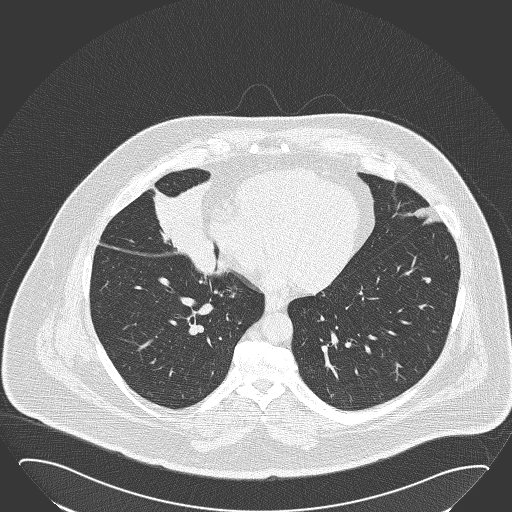
Low-dose screening chest CT, one axial slice; position 65 of 168 along the scan axis; reconstruction kernel B50f; 120 kVp; lung window (W 1500 / L -600 HU); 2 mm slice thickness; 512 × 512 image matrix.
Outlined on this slice (outlined manually by an expert reader):
- lesion 1 (tumor, hilum of right lung): box from (x=153, y=180) to (x=218, y=276) px